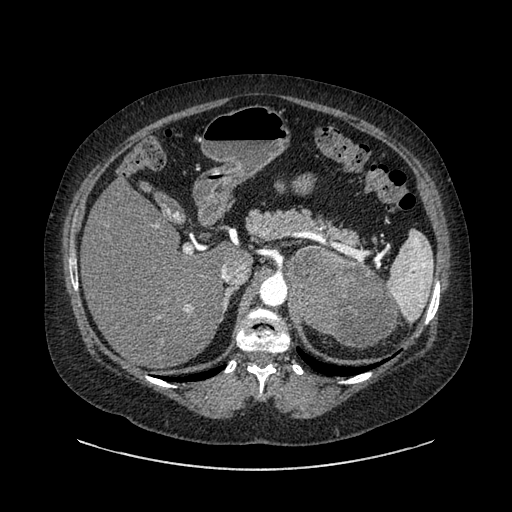
Contrast-enhanced abdominal CT, one axial slice; slice 591 of 769 in the series (ordered by position); reconstruction kernel SOFT; 120 kVp; intravenous contrast given; soft-tissue window (W 400 / L 40 HU); 0.62 mm slice thickness; 512 × 512 image matrix. Patient: female, 61 years. Case-level facts recorded for this patient, not image findings: diagnosis: adrenocortical carcinoma; tumour side: left adrenal; tumour size at pathology: 13 cm; Ki-67 index: 79 %; stage (as recorded): 2.
Structures marked on this image (semi-automatically segmented with operator editing):
- mass: box from (x=287, y=248) to (x=394, y=346) px